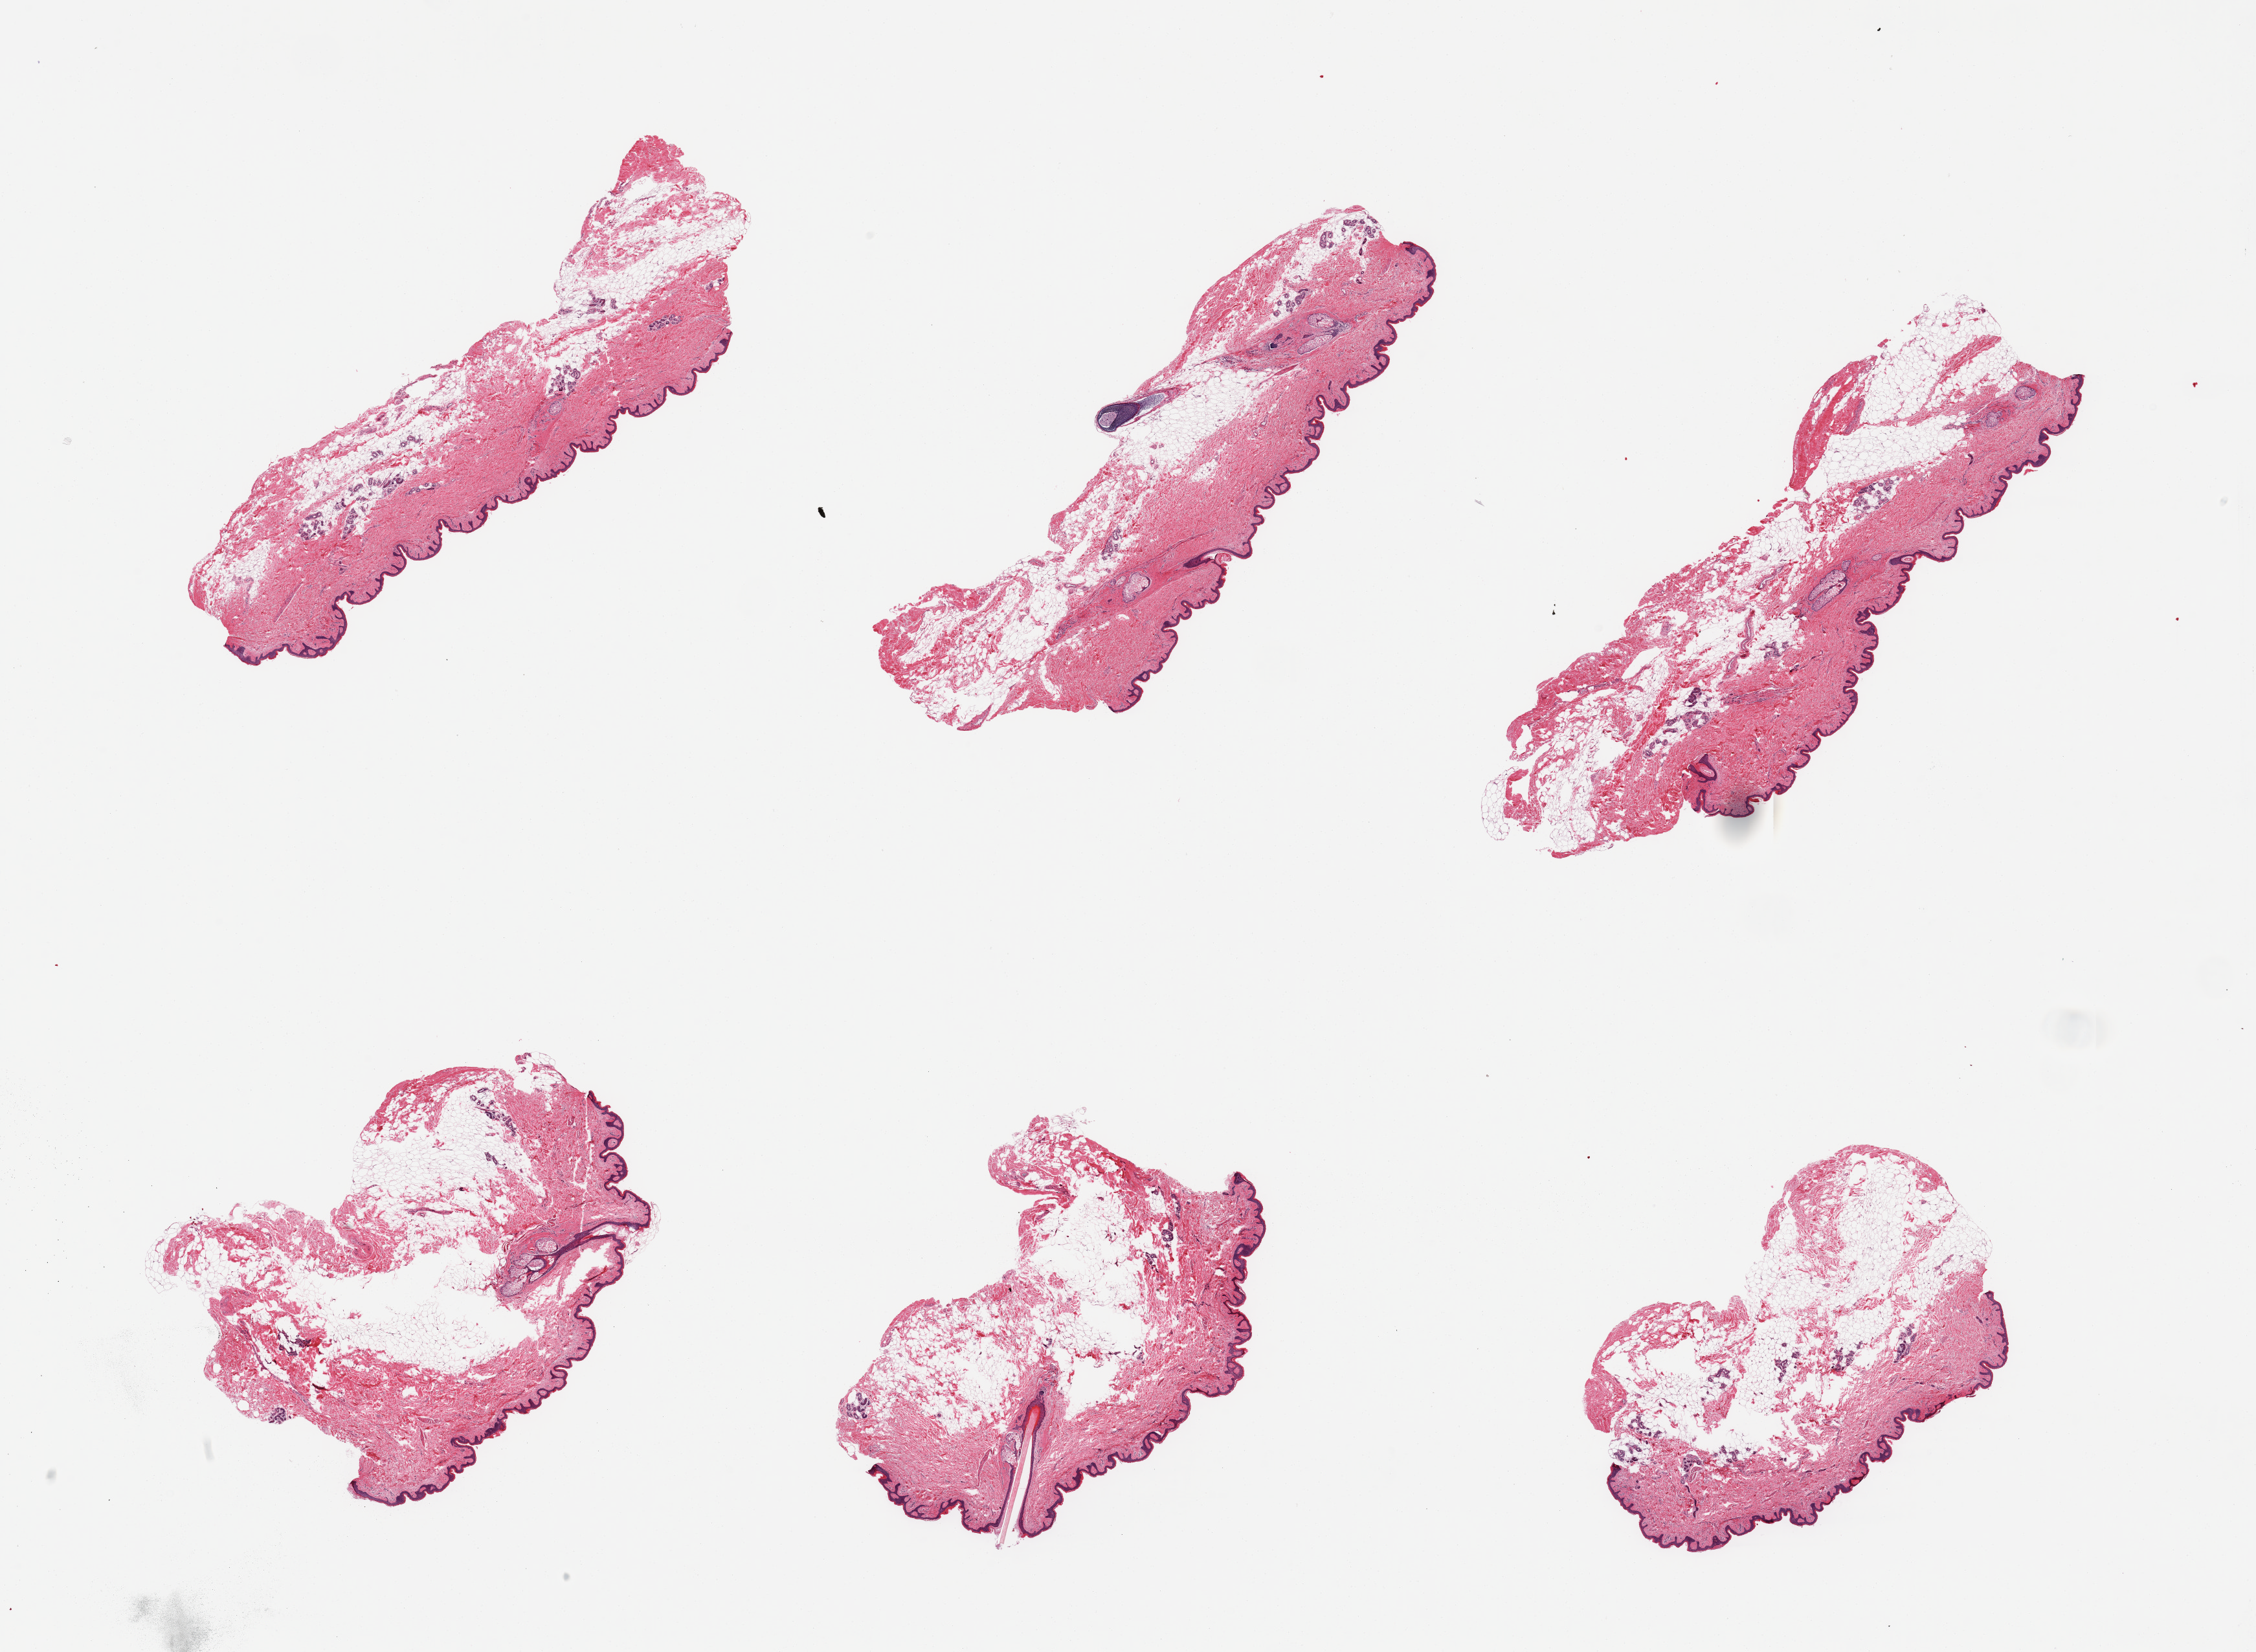
Whole-slide image, haematoxylin and eosin stain — low-resolution overview of the scanned area, about 27.6 x 20.2 mm. PAXgene-fixed, paraffin-embedded tissue. Section of skin of suprapubic region (target tissue). Tissue donor sample. Donor: male.
Pathologist's review note for this sample: 6 pieces, moderate interstitial dermal fat; squamous epithelium is ~30-40 microns.